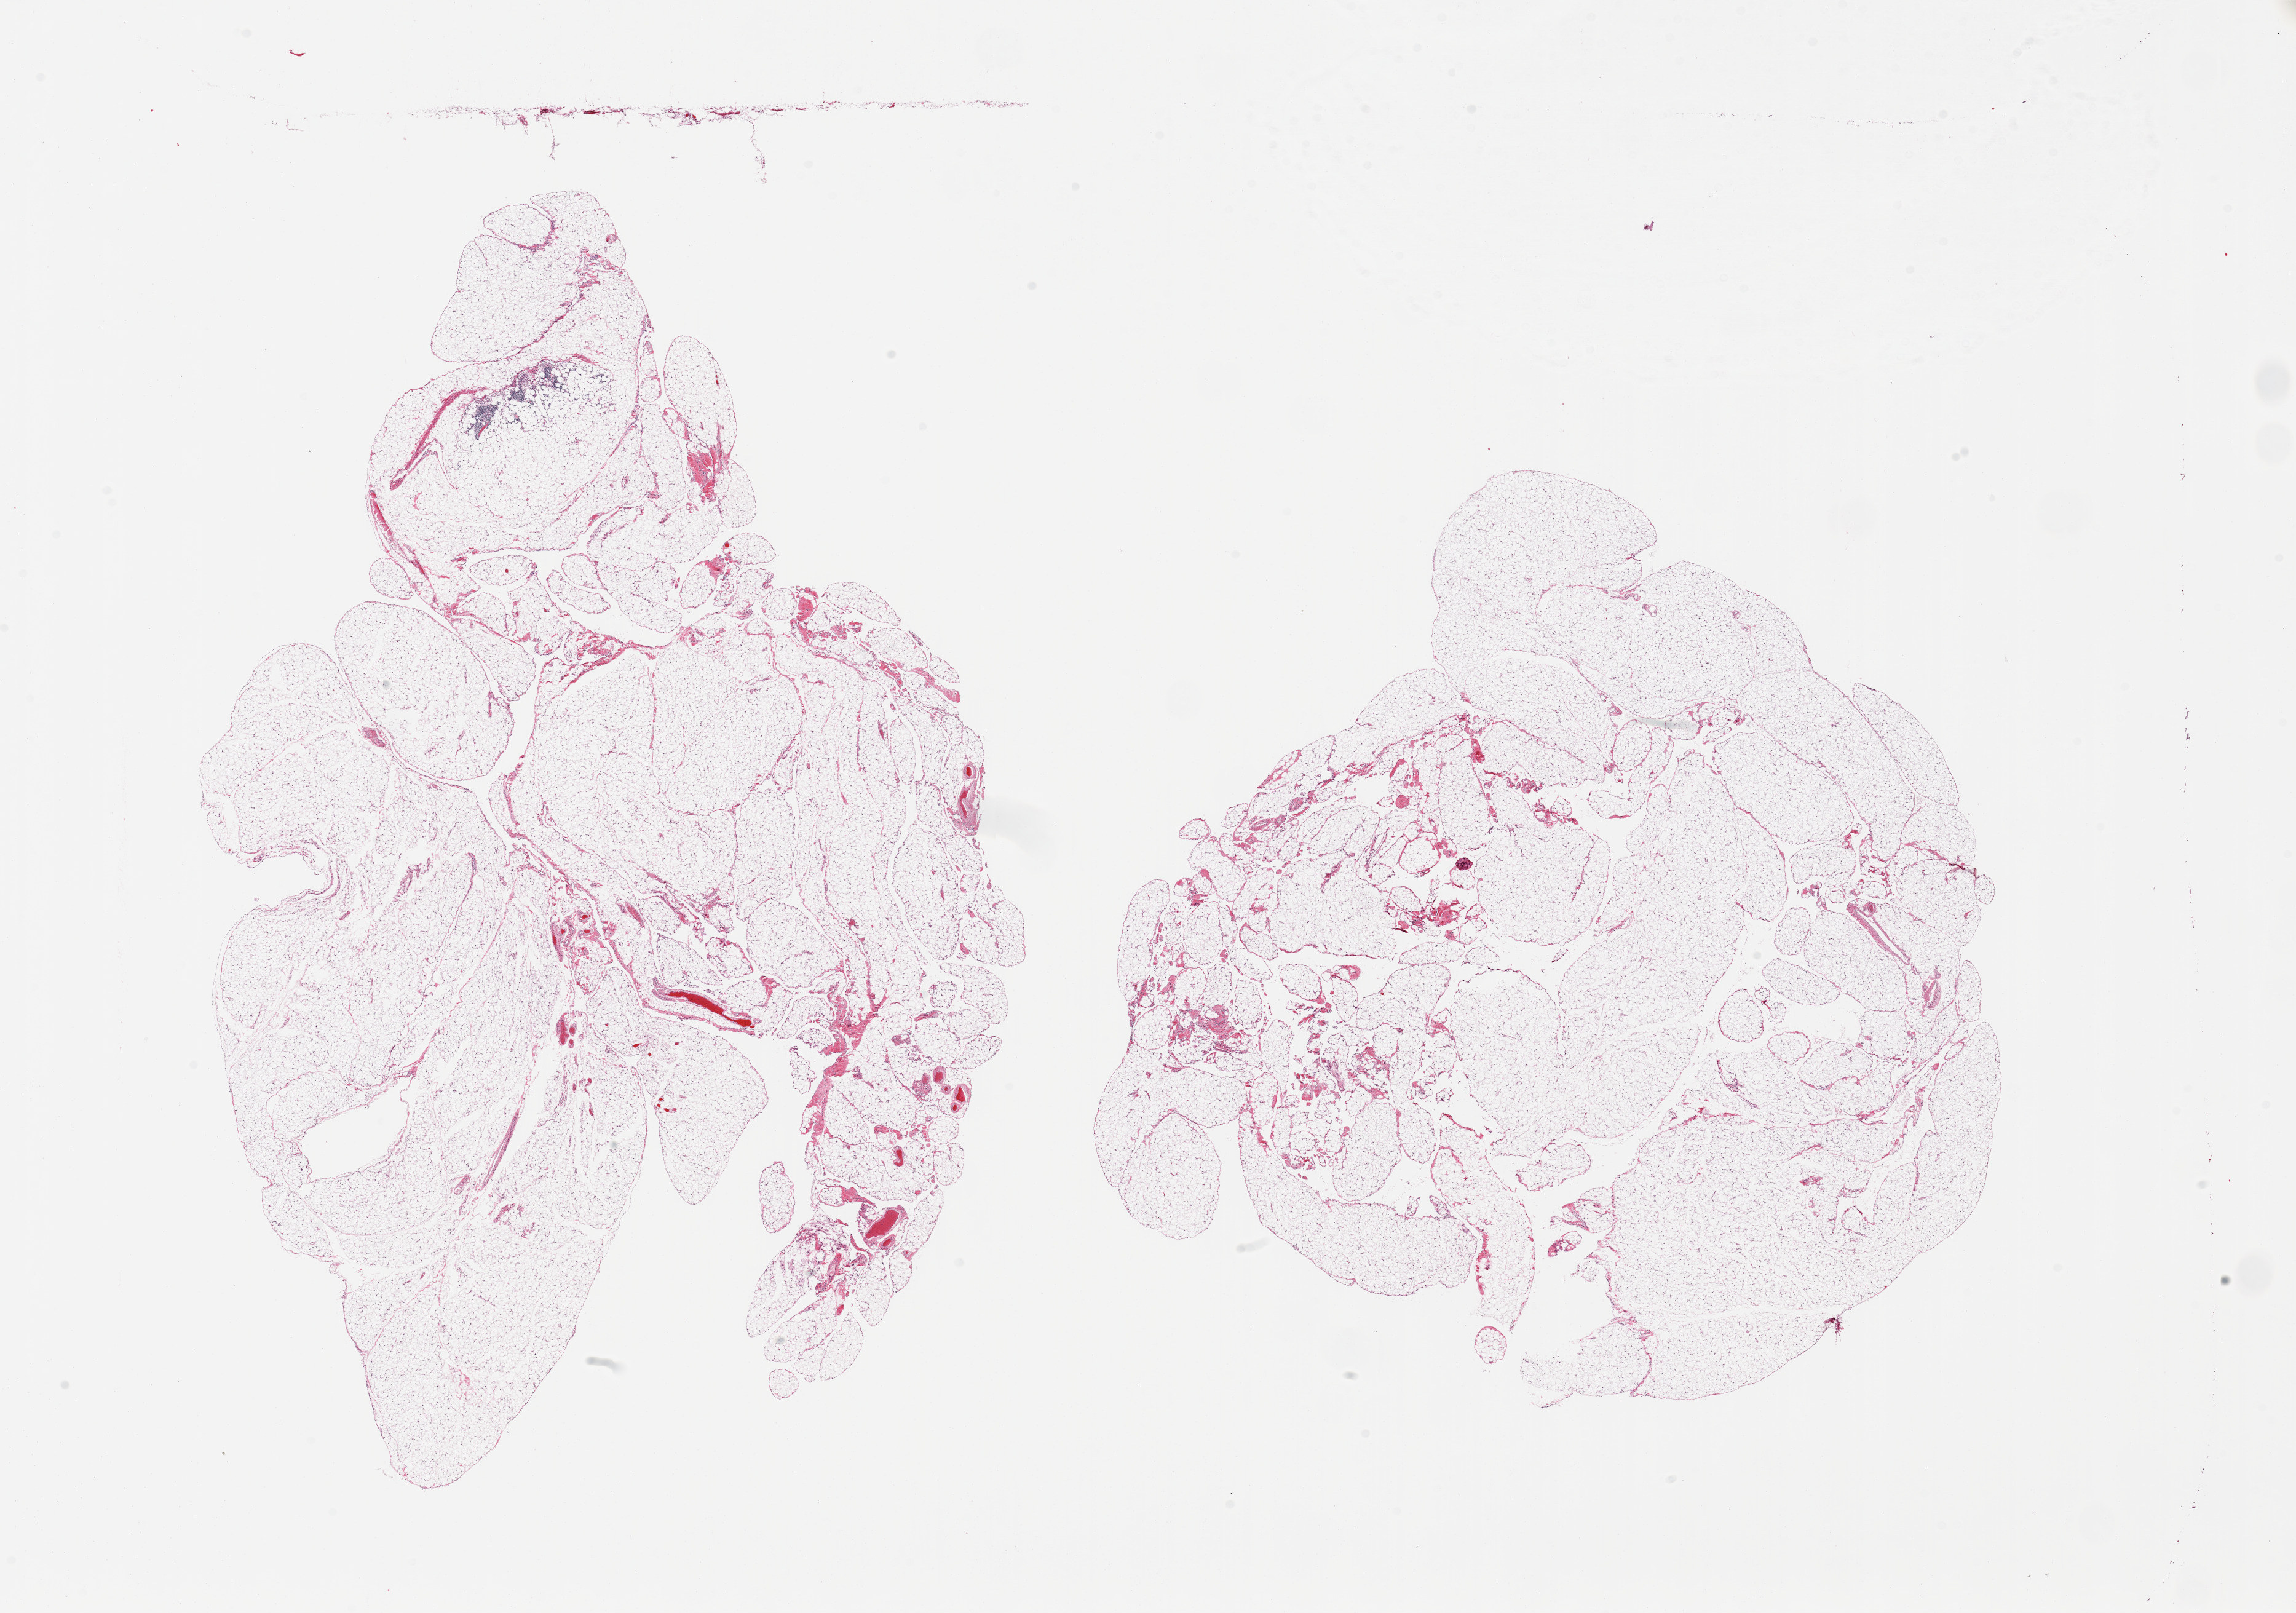
H&E whole-slide image, brightfield — whole scanned area (about 29.5 x 20.7 mm) shown as a low-resolution overview. PAXgene-fixed paraffin-embedded (PFPE) section. Target tissue: omentum. Tissue donor sample. Male donor.
Reviewer comment on this tissue sample: 2 pieces minimal fascia.